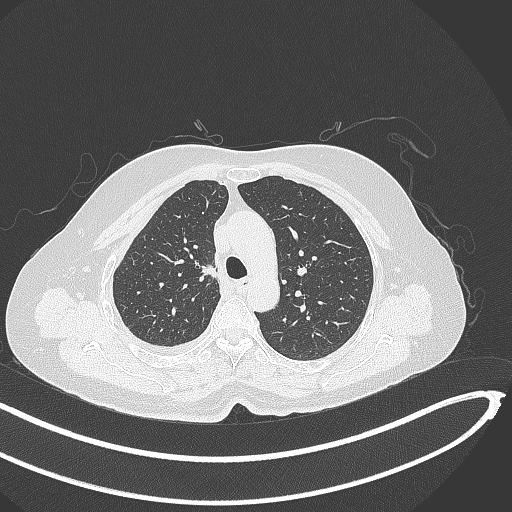
Chest CT, one axial slice; position 271 of 345 along the scan axis; reconstruction kernel B70f; lung window (W 1500 / L -600 HU); 1 mm slice thickness; 512 × 512 image matrix, field of view 400 × 400 mm. Patient: female, 64 years. From the clinical record (not read from this slice): clinical TNM (as recorded): T1b N0 M1.
Structures marked on this image (bounding box drawn by a radiologist):
- lung tumour (recorded histology: adenocarcinoma): bounding box [x1, y1, x2, y2] px = [195, 255, 221, 284]